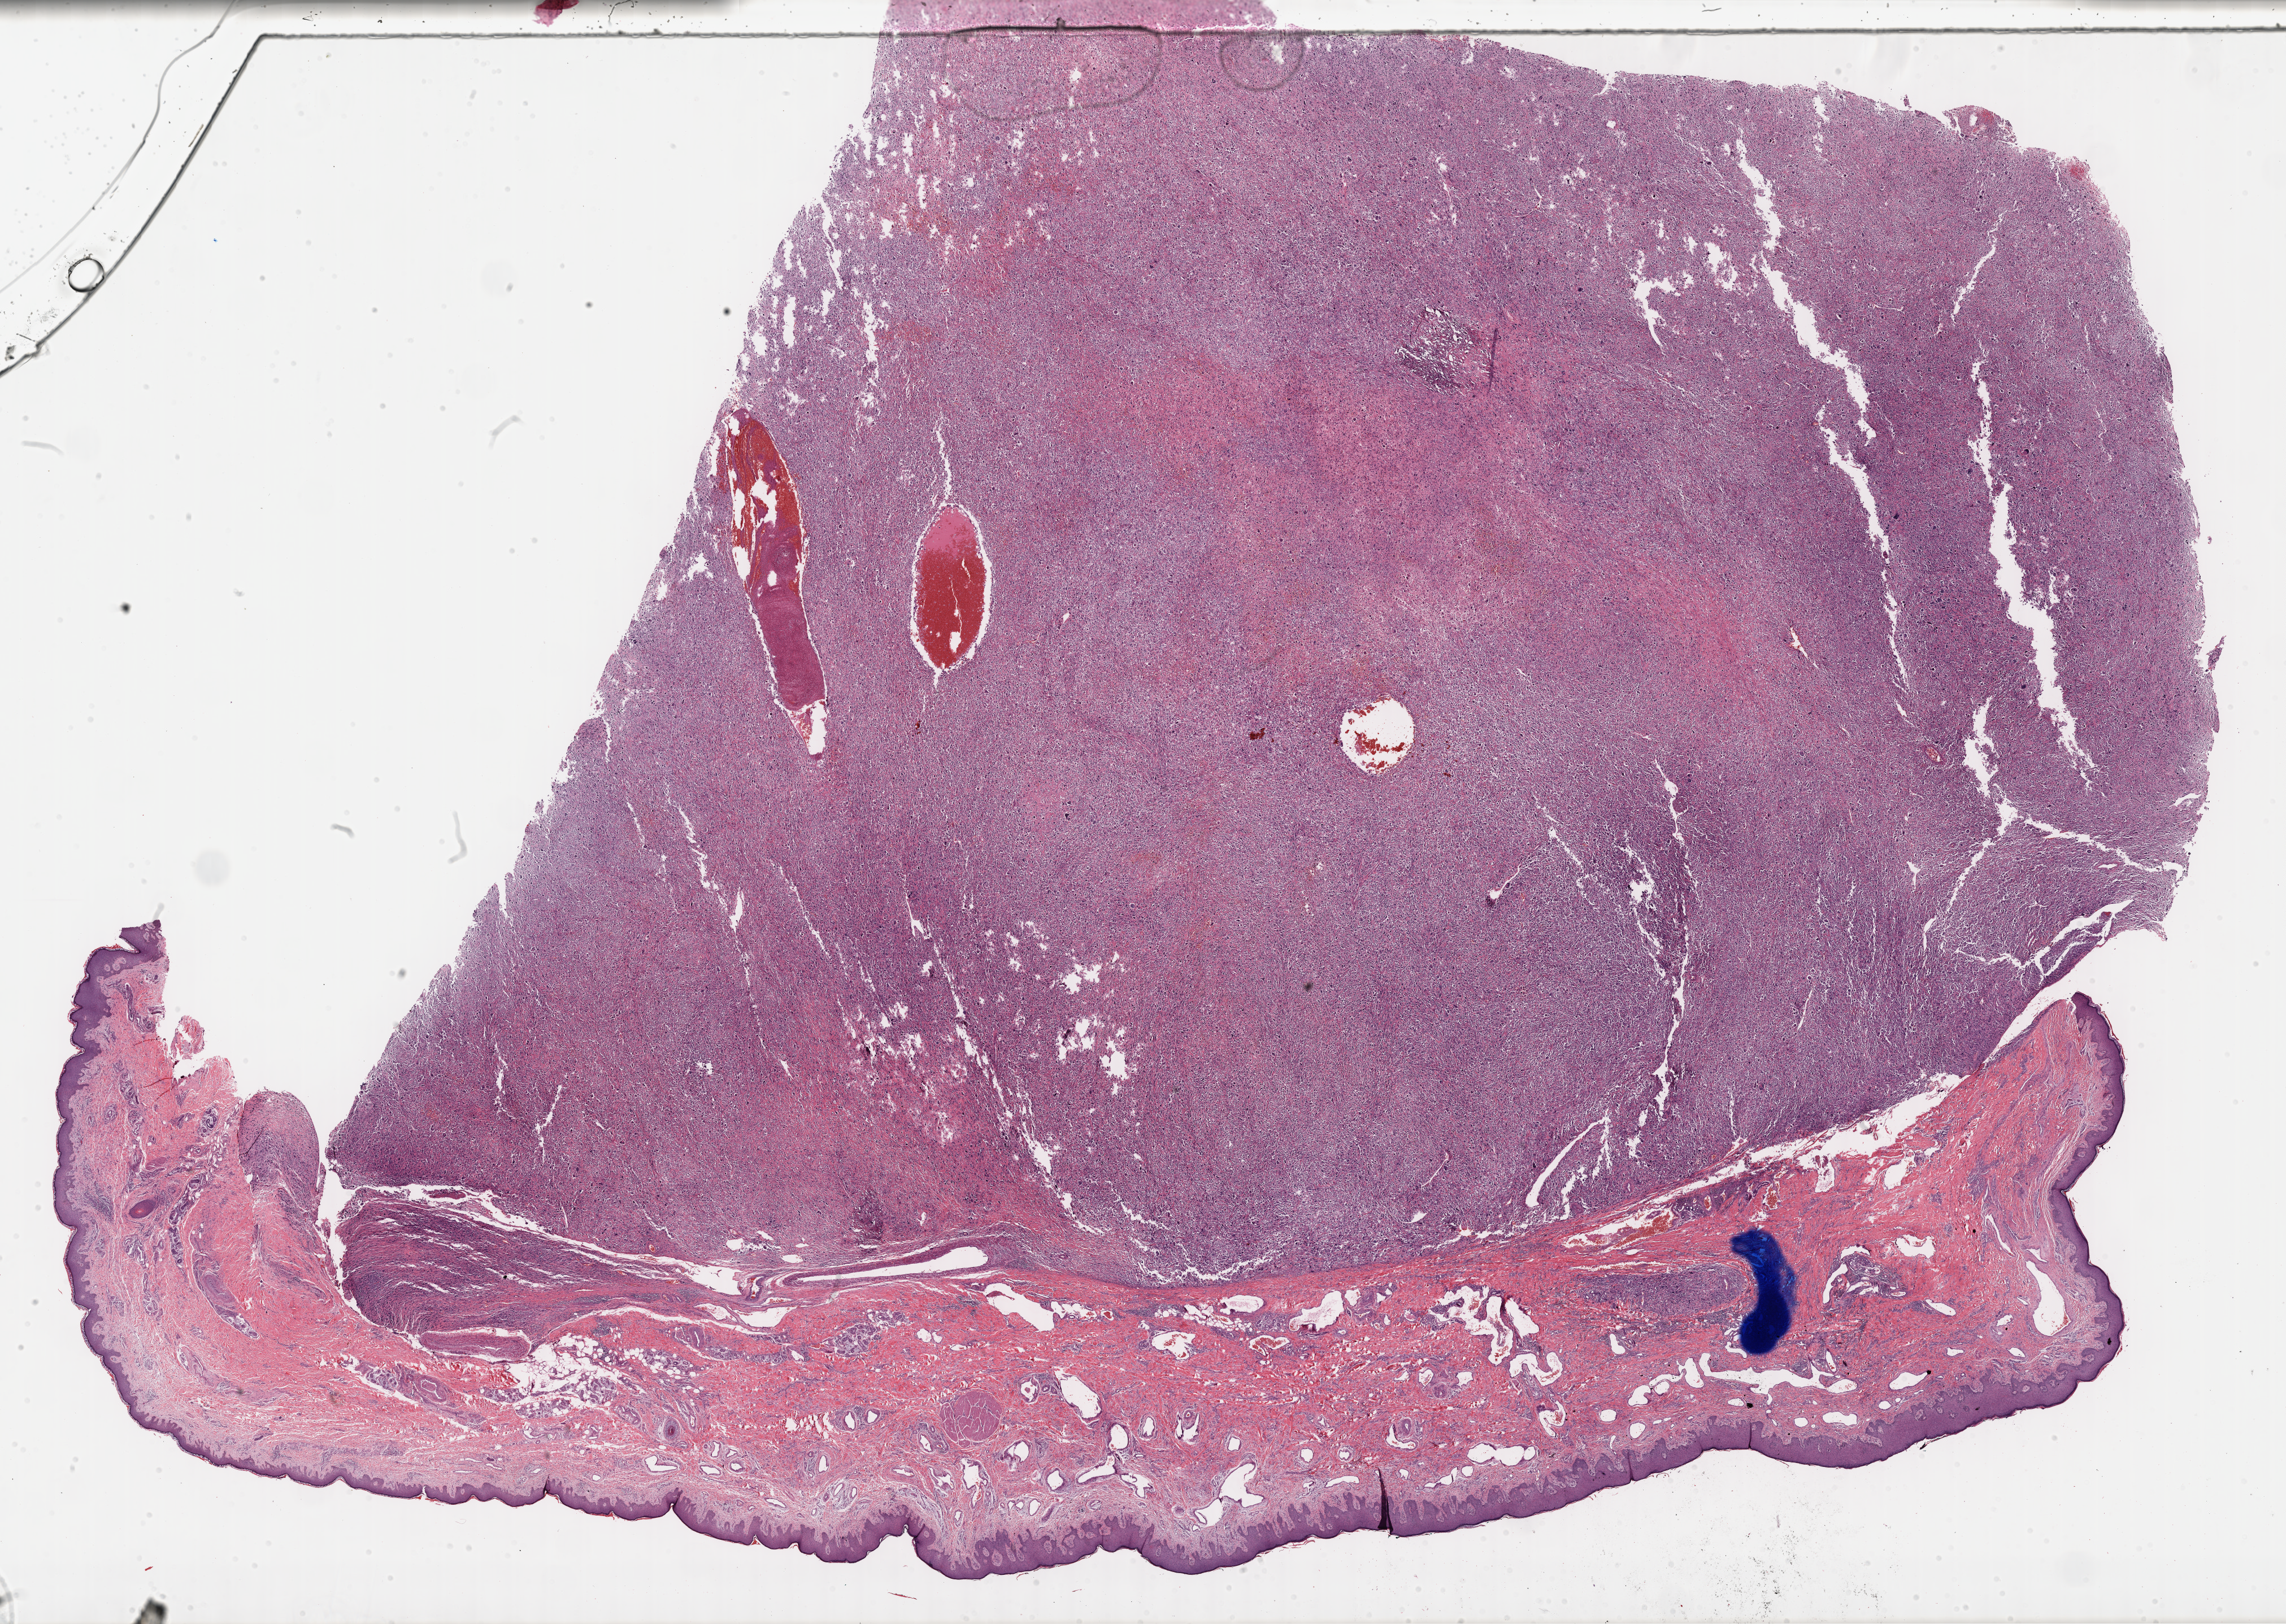
H&E-stained whole-slide image, a low-resolution overview of the entire scanned area, about 32.7 x 23.2 mm (slide scanned at 40x). FFPE section. Connective, subcutaneous and other soft tissues, primary tumour sample. Patient: female, age at initial diagnosis 78 years.
Pathologic diagnosis: Malignant fibrous histiocytoma (connective, subcutaneous and other soft tissues of lower limb and hip).